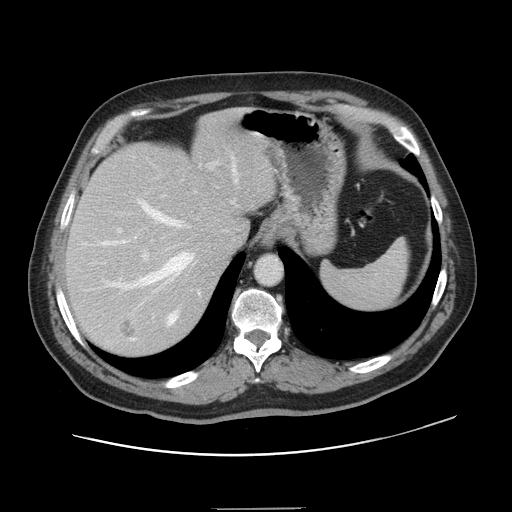
Contrast-enhanced abdominal CT, one axial slice; intravenous contrast given; soft-tissue window (W 400 / L 40 HU); 512 × 512 image matrix, field of view 402 × 402 mm. Male patient, age 62 years. Case-level facts recorded for this patient, not image findings: diagnosis: colorectal cancer liver metastases, imaged before liver resection; multiple liver metastases: yes; largest metastasis: 2.7 cm; disease in both lobes: no.
Outlined on this slice (expert manual segmentation):
- hepatic veins: bounding box <100,164,238,325> (left, top, right, bottom; pixels)
- liver: <67,114,276,356>
- planned liver remnant (the part of the liver to remain after resection): <67,113,275,277>
- portal vein (with intrahepatic branches): <118,162,218,340>
- liver metastasis: <120,320,137,338>
- liver metastasis: <167,161,180,174>